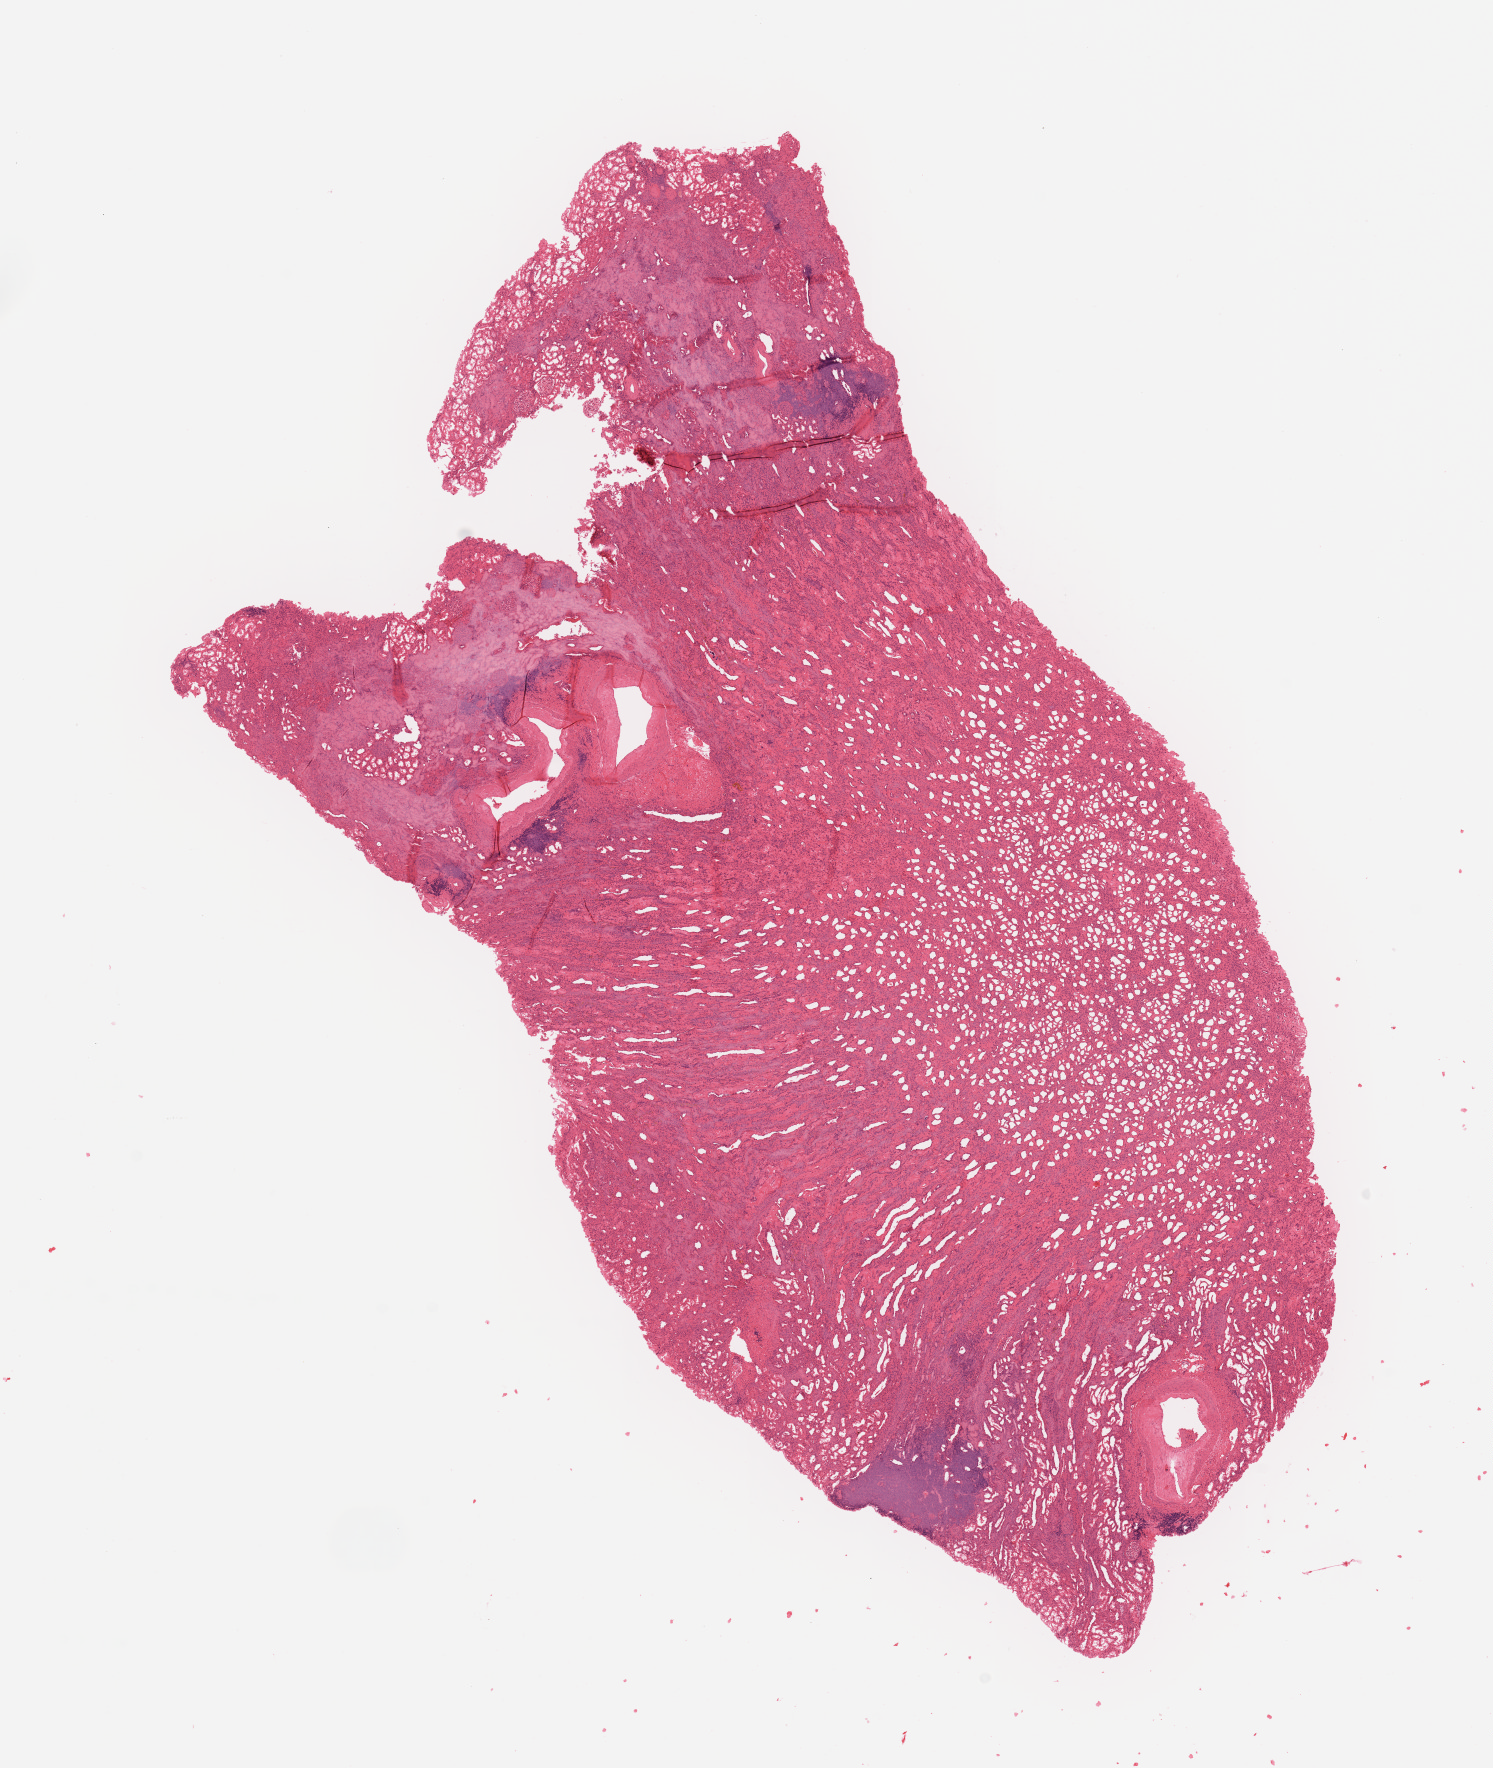
Digitized Hematoxylin and eosin (H&E) stained tissue section (whole slide) — shown as a low-resolution overview of the whole scanned area (about 11.8 x 14.0 mm), normal (non-tumour) tissue sample, kidney. Patient: male, age 68 years.
This section: normal (non-tumour) tissue from the same patient. Patient diagnosis: Renal cell carcinoma, NOS.